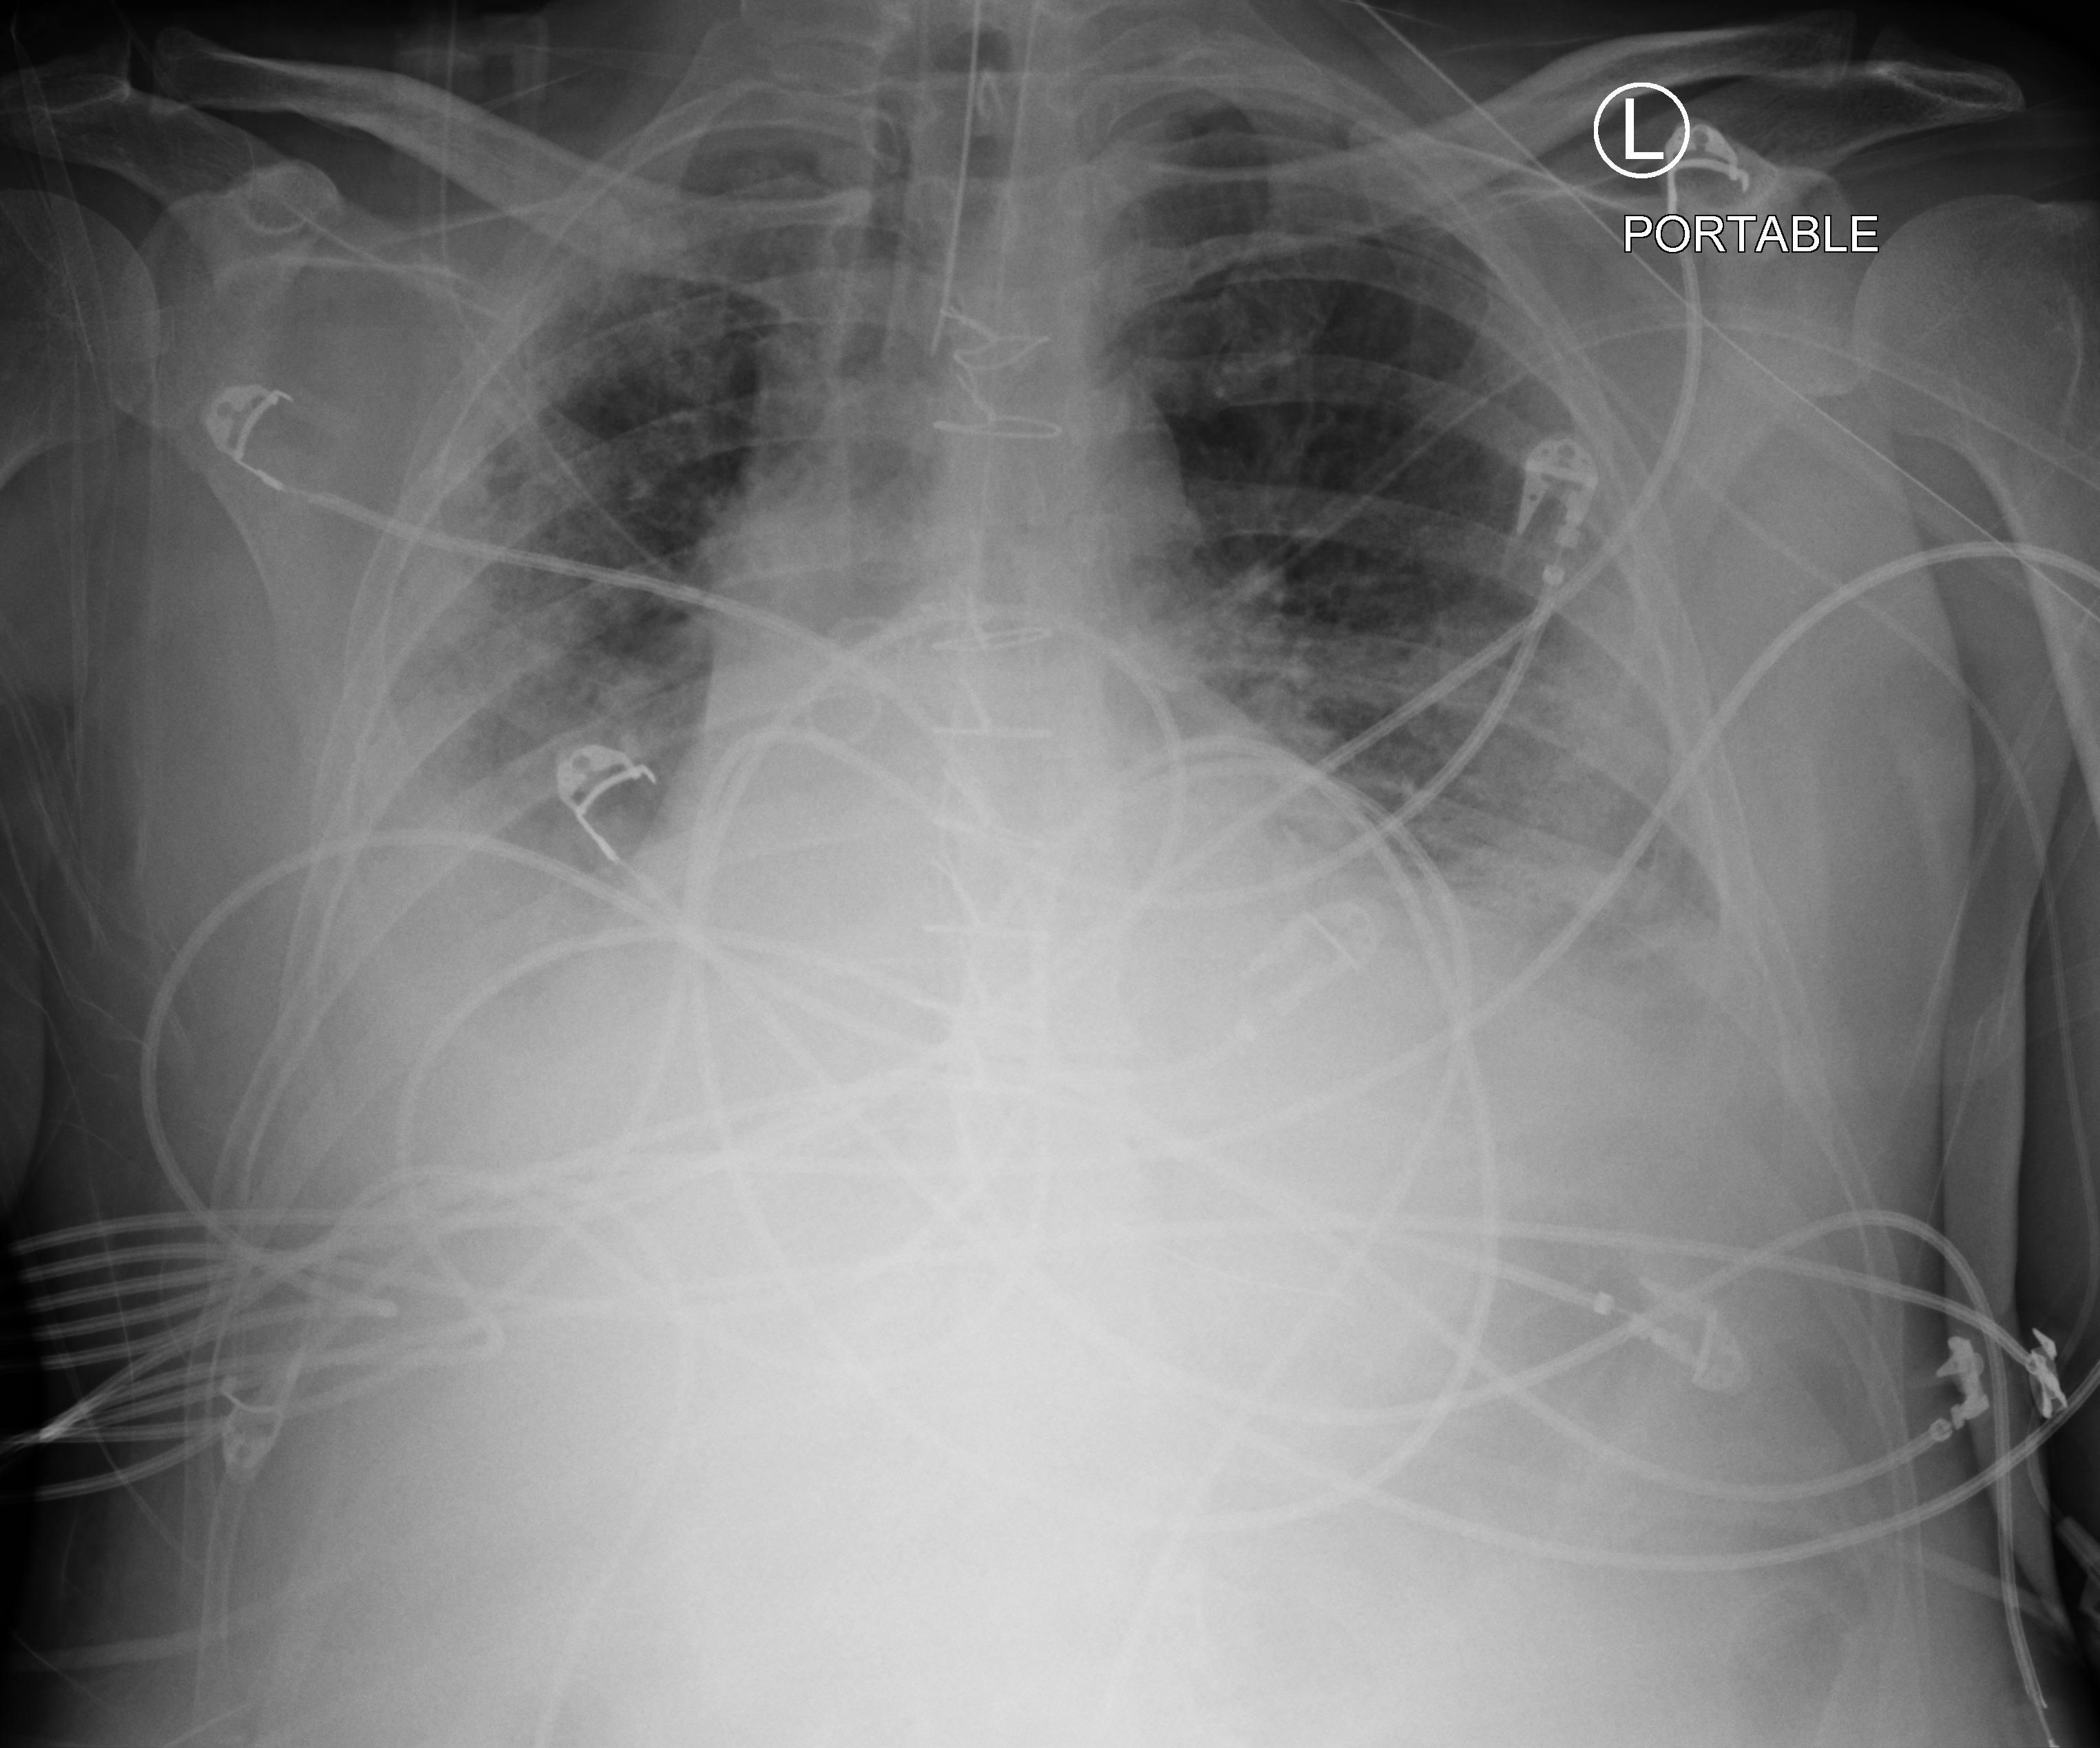
Bedside chest radiograph (computed radiography); anteroposterior (AP) projection. Patient hospitalised with COVID-19; male, aged 18–59 years.
Hospital-stay facts (about this admission, not read from this image; timing relative to this image not recorded):
- length of hospital stay: 63 days
- admitted to intensive care during this hospital stay: yes
- mechanically ventilated during this hospital stay: yes